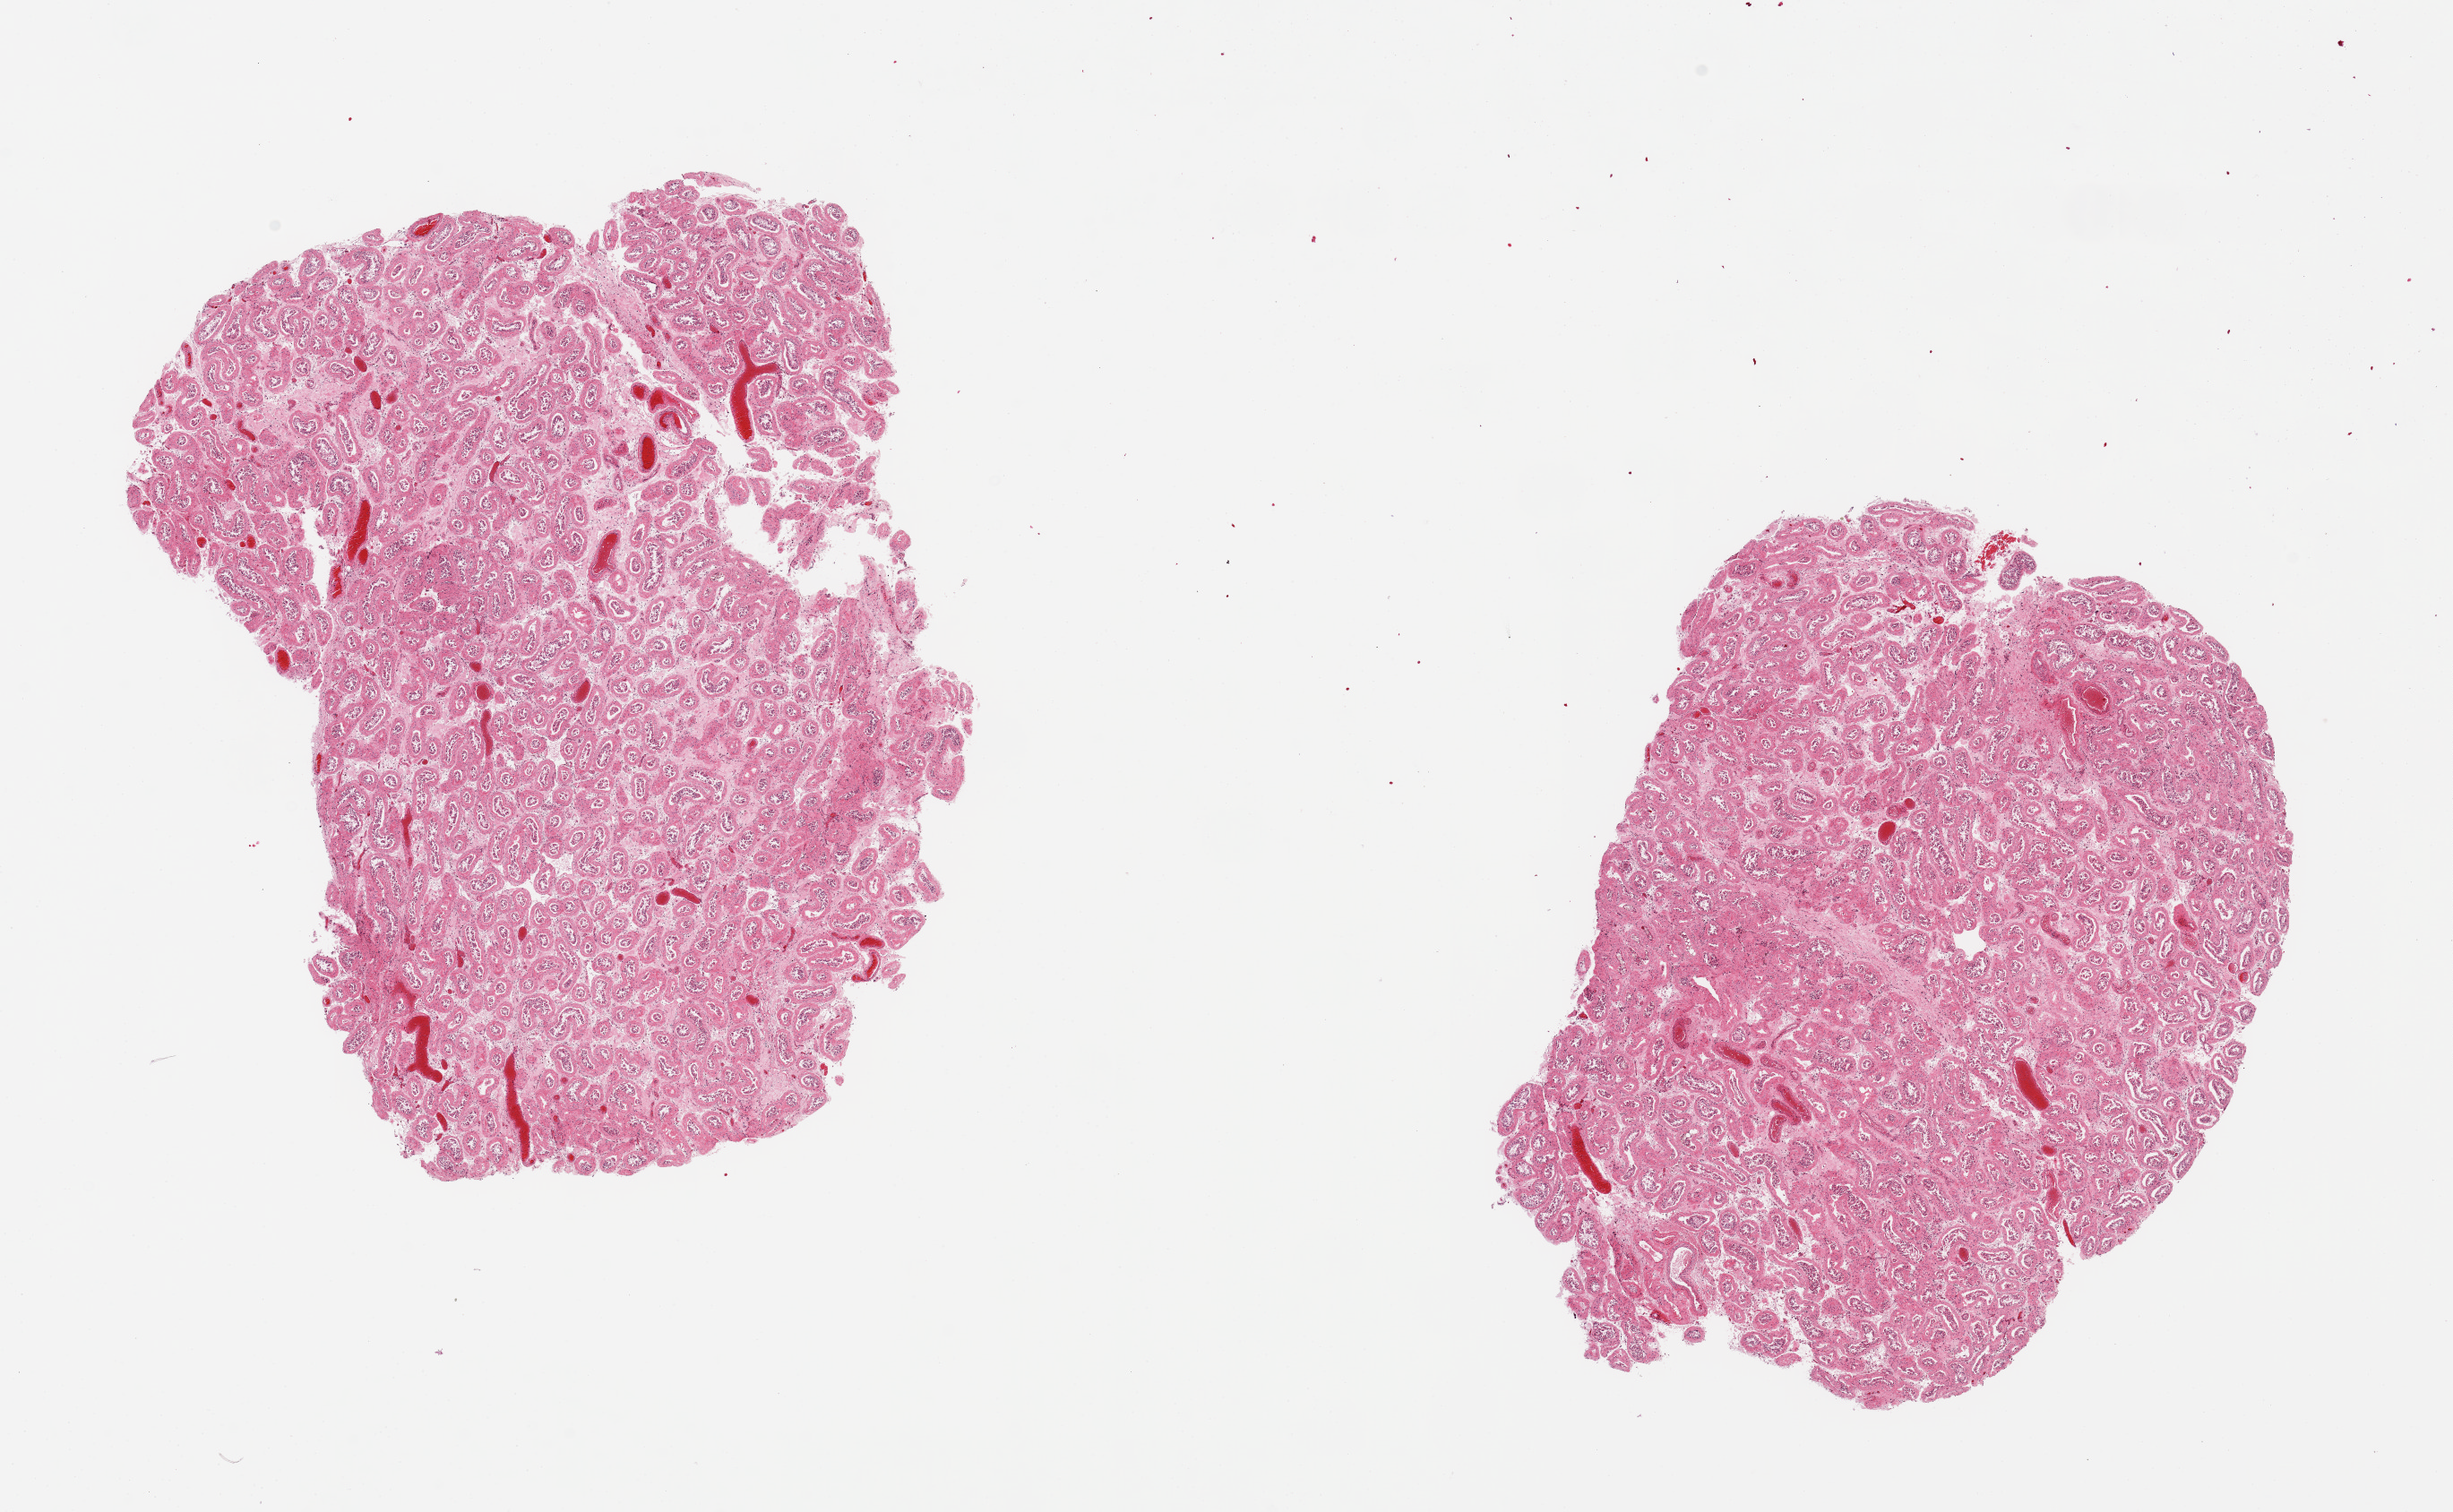
Digitized haematoxylin and eosin-stained section — a low-resolution overview of the entire scanned area, about 21.7 x 13.4 mm. PAXgene-fixed, paraffin-embedded tissue. Target tissue: testis. Donor tissue sample. Donor: male.
Pathologist's review note for this sample: 2 pieces 8.5x7 & 8x6mm; tubules badly autolyzed.